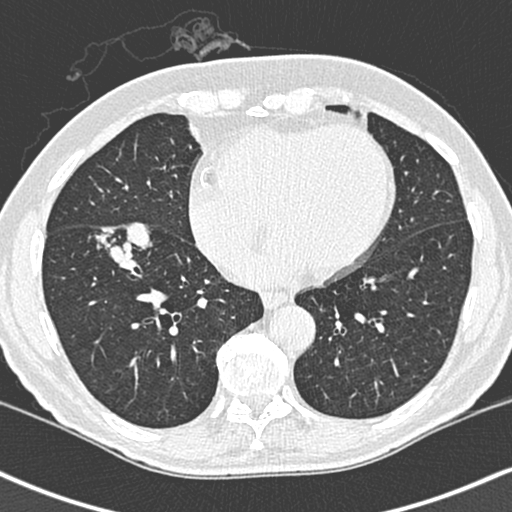
Low-dose screening chest CT, one axial slice; position 102 of 248 along the scan axis; 120 kVp; lung window (W 1500 / L -600 HU); 512 × 512 image matrix.
Structures marked on this image (expert manual segmentation):
- lesion 1 (tumor, lower lobe of right lung): bounding box (x1, y1, x2, y2) in pixels: (95, 184, 152, 231)